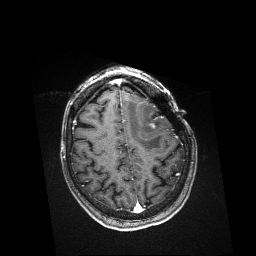
Brain MRI from a brain-tumour surgery series, one axial slice. T1-weighted post-contrast. 256 × 256 image matrix, field of view 256 × 256 mm. From the clinical record (not read from this slice): histopathology: Metastatic Melanoma; tumour location: Left Frontal.
Outlined on this slice (outlined manually by an expert reader):
- residual tumour: bounding box (x1, y1, x2, y2) in pixels: (148, 122, 156, 129)